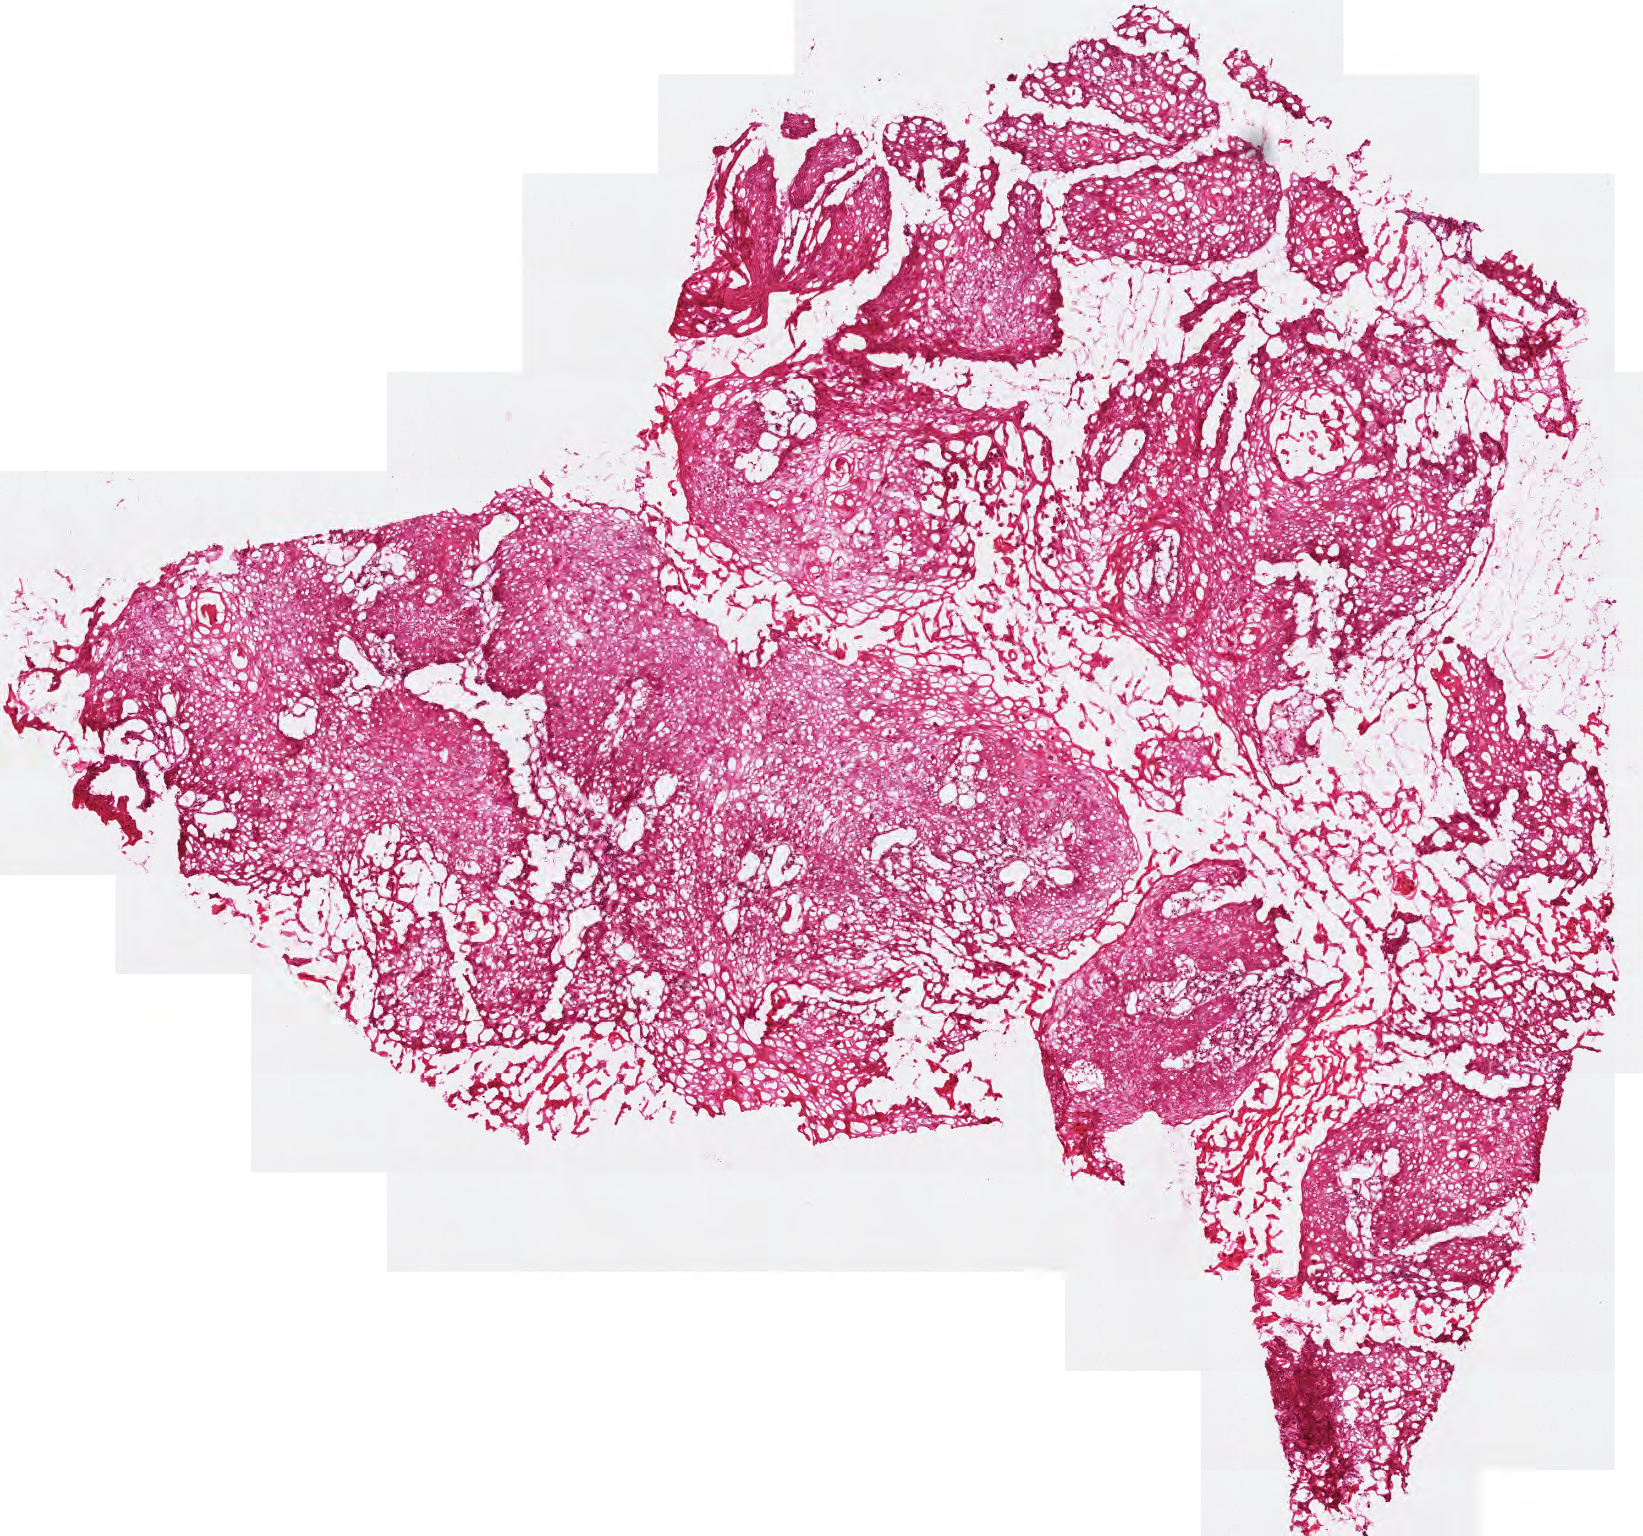
Digitized H&E-stained tissue section (whole slide) — shown as a low-resolution overview of the whole scanned area (about 3.3 x 3.1 mm); frozen section from the top of the tissue portion; primary tumour sample from the head and neck. Patient: male, age at initial diagnosis 60 years. Histologic grade: G2 (moderately differentiated). Pathologist review of this section (percent, as recorded): tumour cells 70%, tumour nuclei 90%, normal cells 0%, stromal cells 30%, necrosis 0%.
* AJCC pathologic stage: IVA (7th edition)
* lymph nodes positive (case pathology): 2 of 49 examined
* pathologic diagnosis: Squamous cell carcinoma, NOS (floor of mouth, NOS)